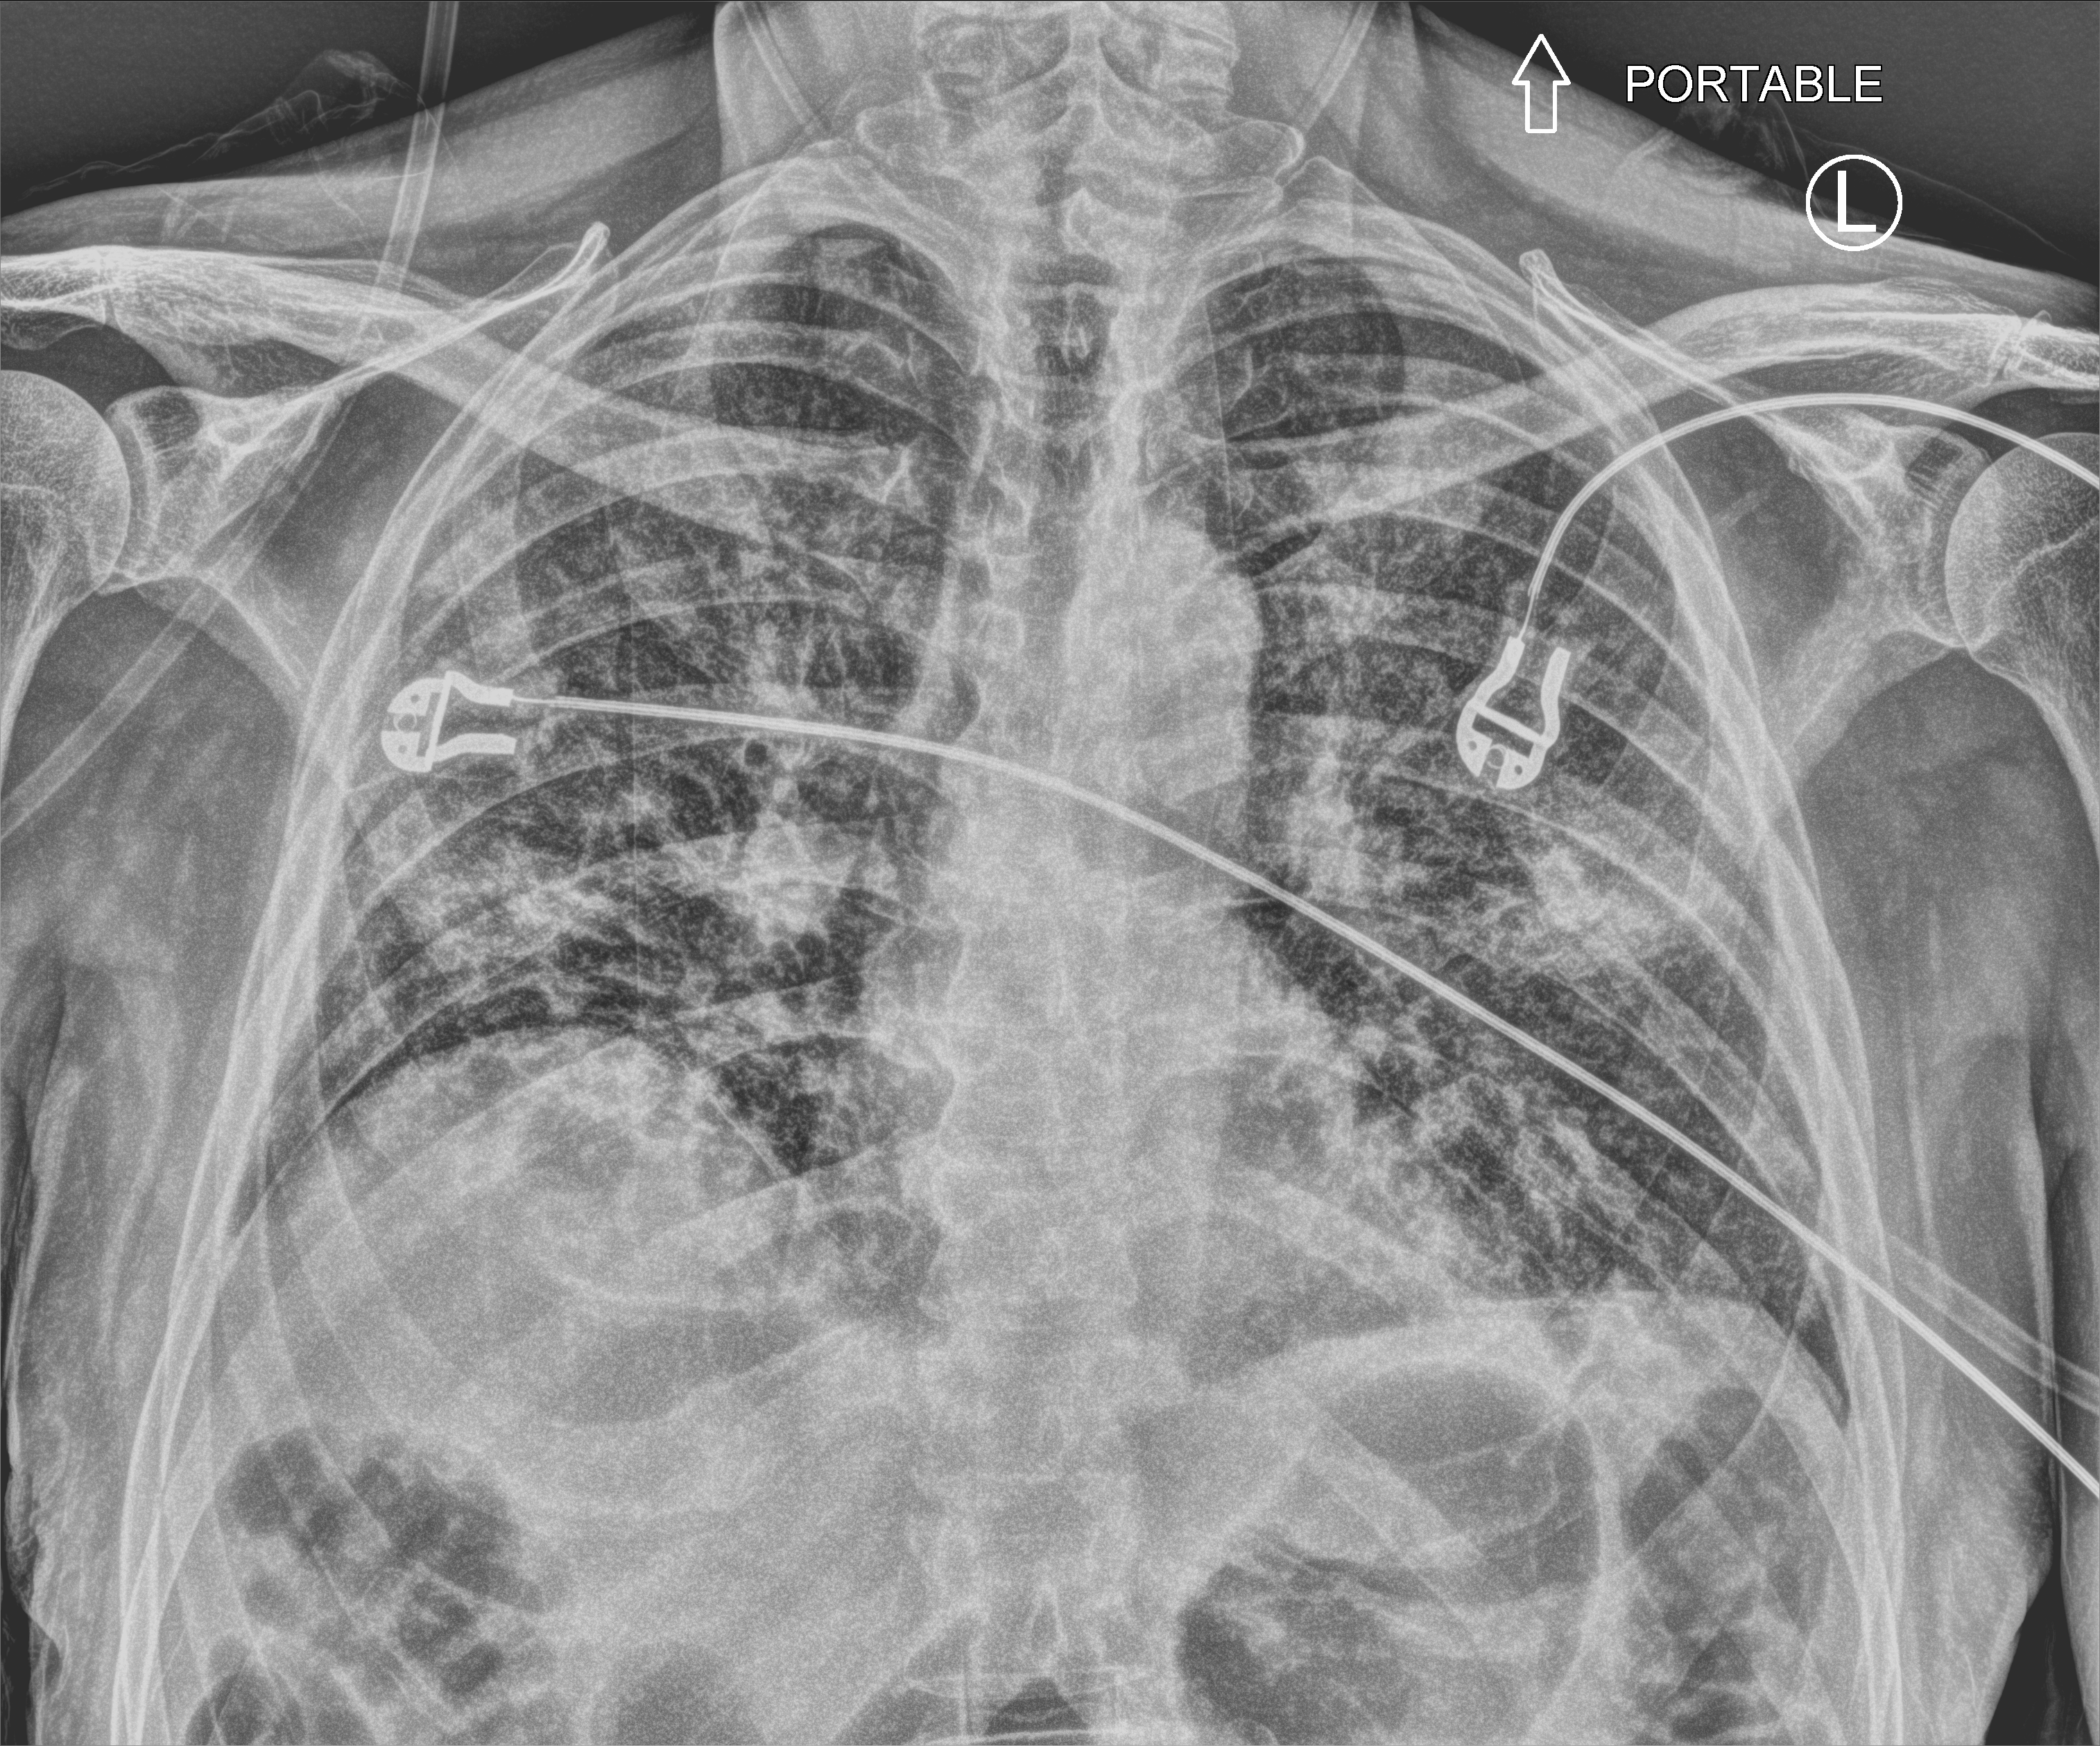
Portable chest radiograph, anteroposterior (AP) projection. Patient hospitalised with COVID-19; male, aged 60–74 years.
Admission-level facts for this patient (not findings on this image; timing relative to this image not recorded): mechanically ventilated during this hospital stay: no; admitted to intensive care during this hospital stay: no; diabetes (admission record): no.